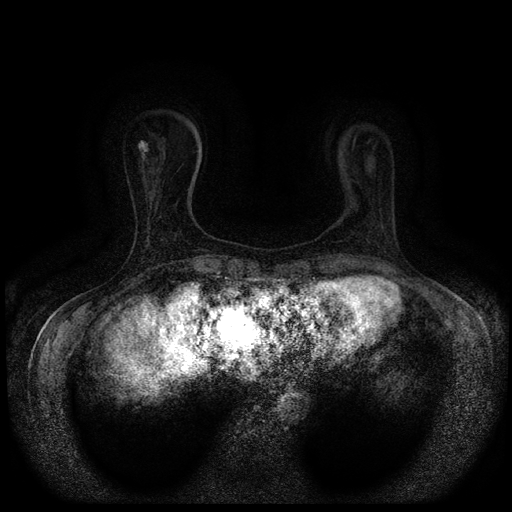
Breast MRI (dynamic contrast-enhanced, multi-phase), one axial slice; slice 22 of 116 in the series (ordered by position); dynamic contrast-enhanced series, time point 2 of 5 at this slice position (early post-contrast); 1.5 T; TE 2.7 ms, TR 5.4 ms; 2 mm slice thickness; 512 × 512 image matrix, field of view 330 × 330 mm. Female patient, age 63 years.
Annotated regions visible in this slice (semi-automatic segmentation, software-assisted and operator-edited):
- breast lesion (labelled benign in the annotation): bounding box <138,140,149,161> (left, top, right, bottom; pixels)